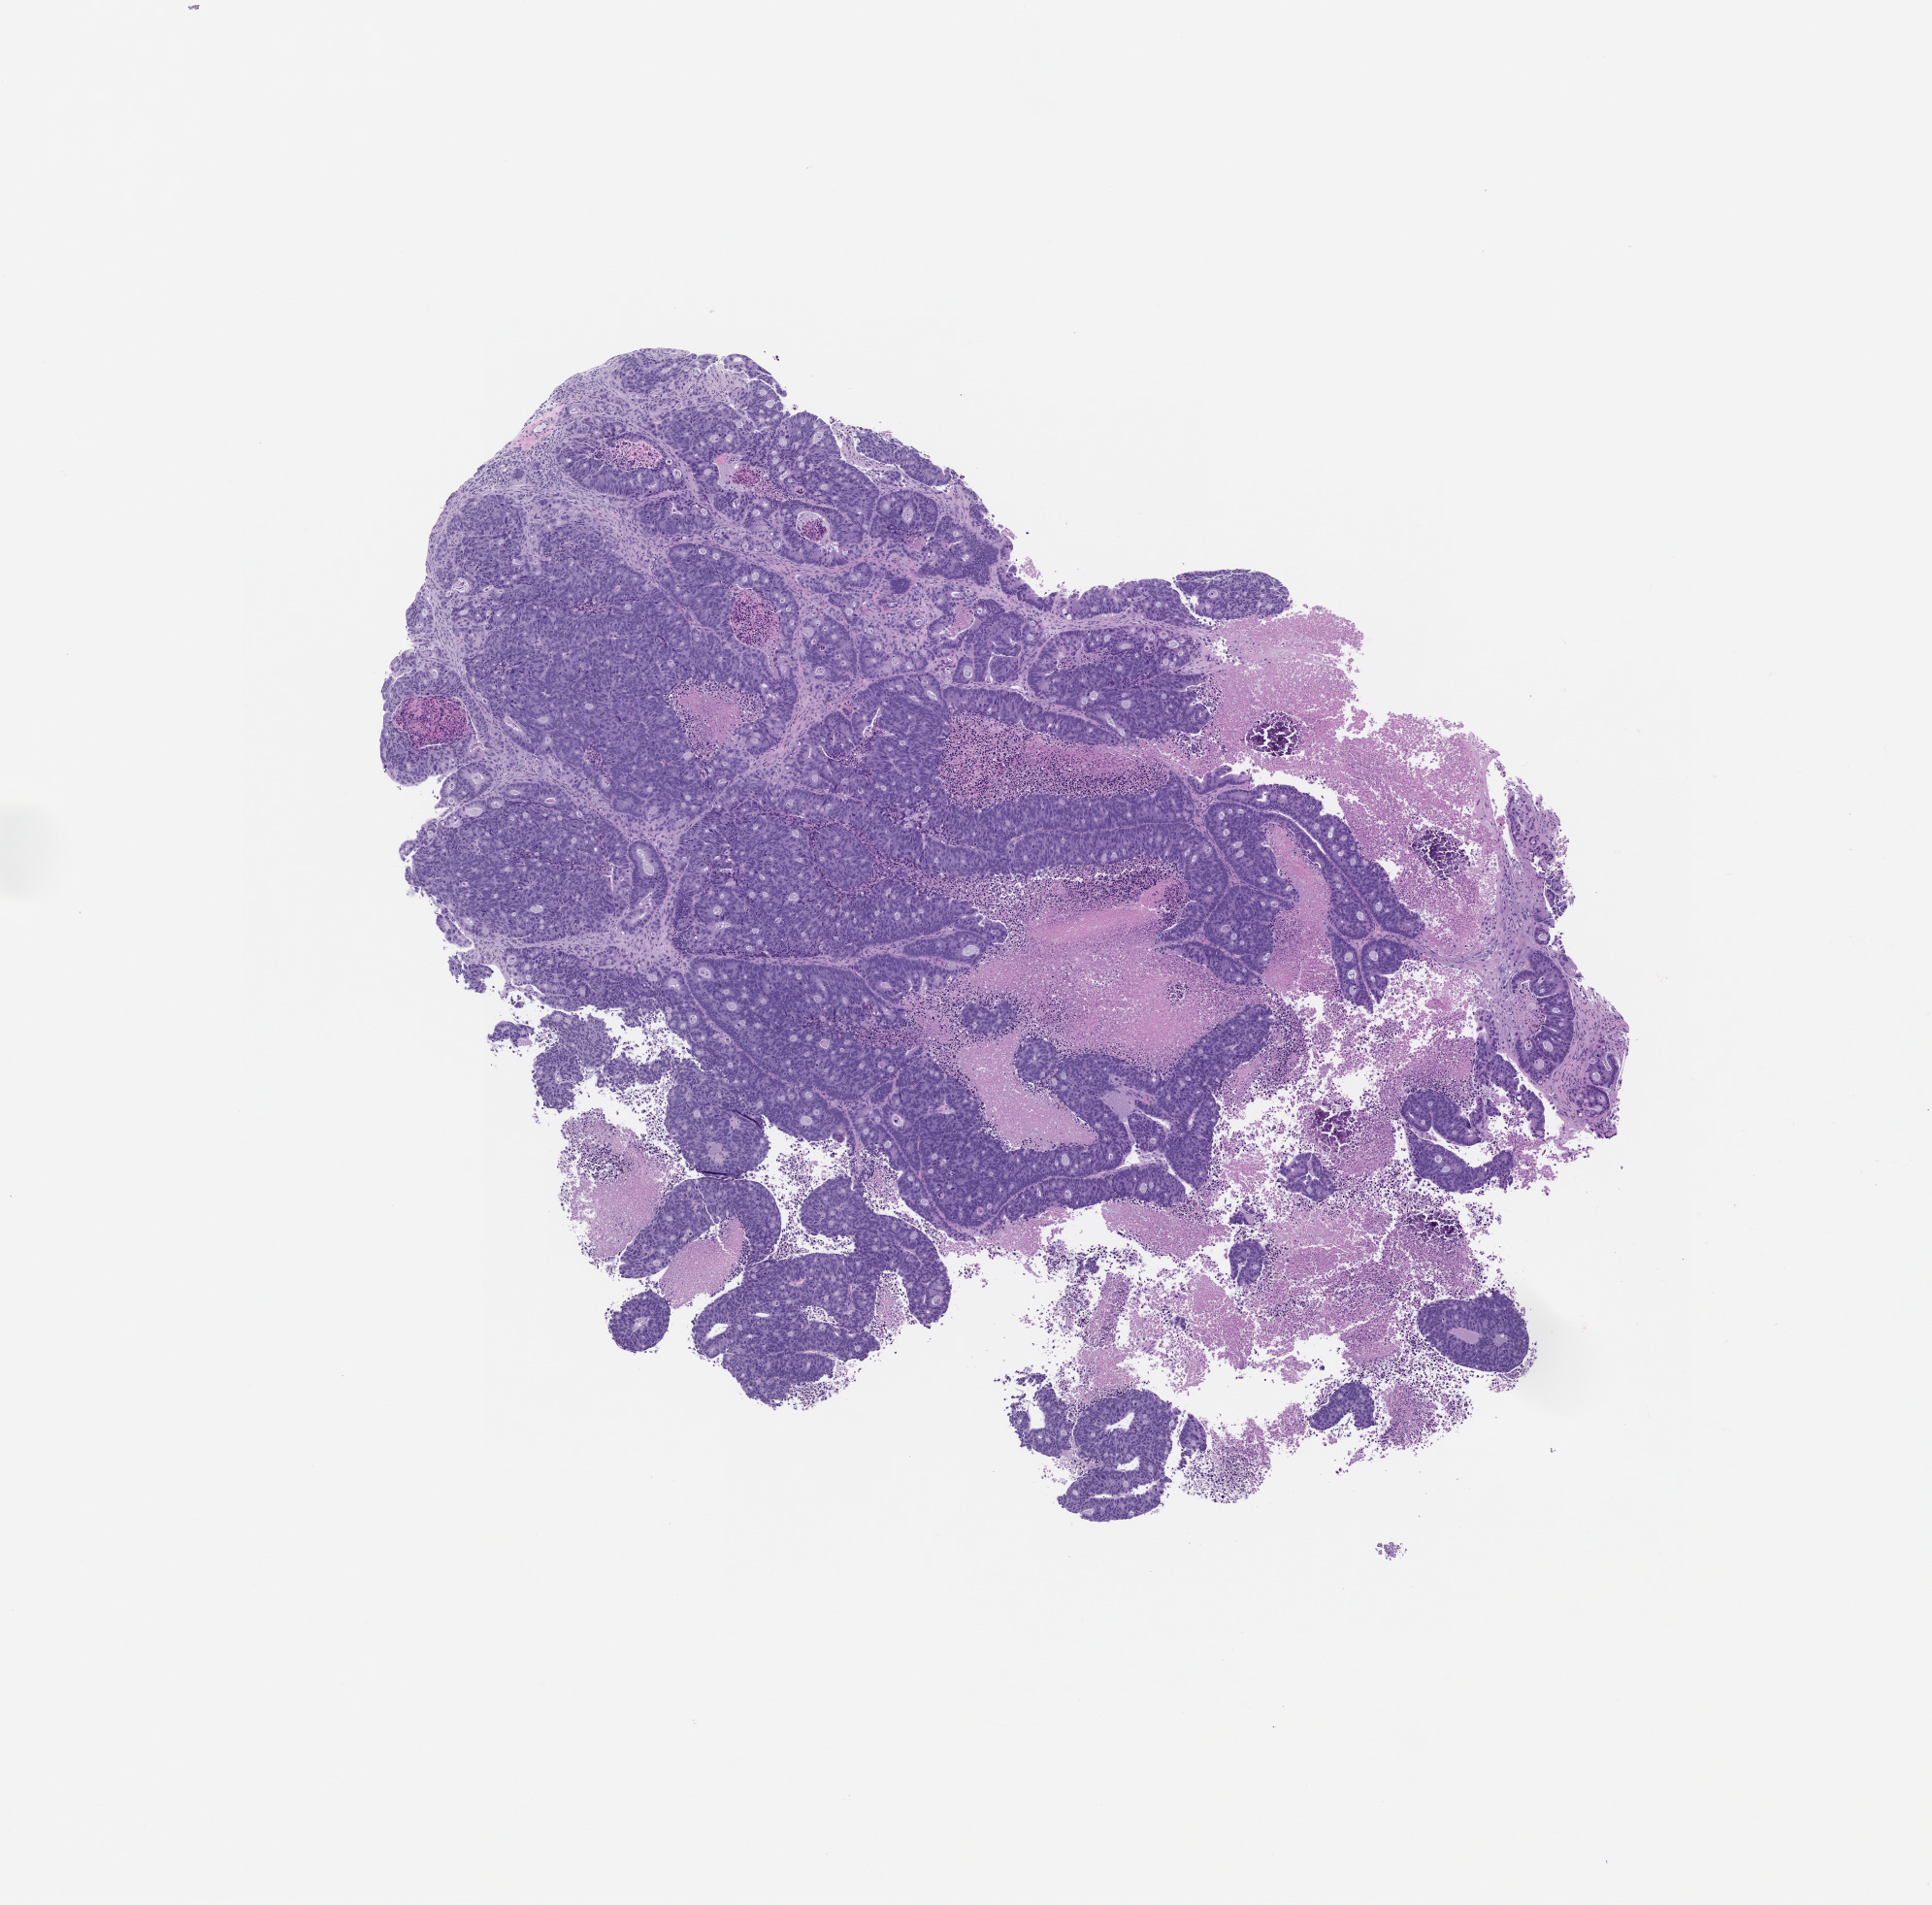
Whole-slide image, H&E: patient-derived xenograft (human tumor grown in a mouse), passage 3, low-resolution overview of the scanned area, about 8.0 x 7.9 mm. Formalin-fixed, paraffin-embedded (FFPE) tissue. Originating tumor site category: colon.
• originating patient diagnosis: Colon Adenocarcinoma